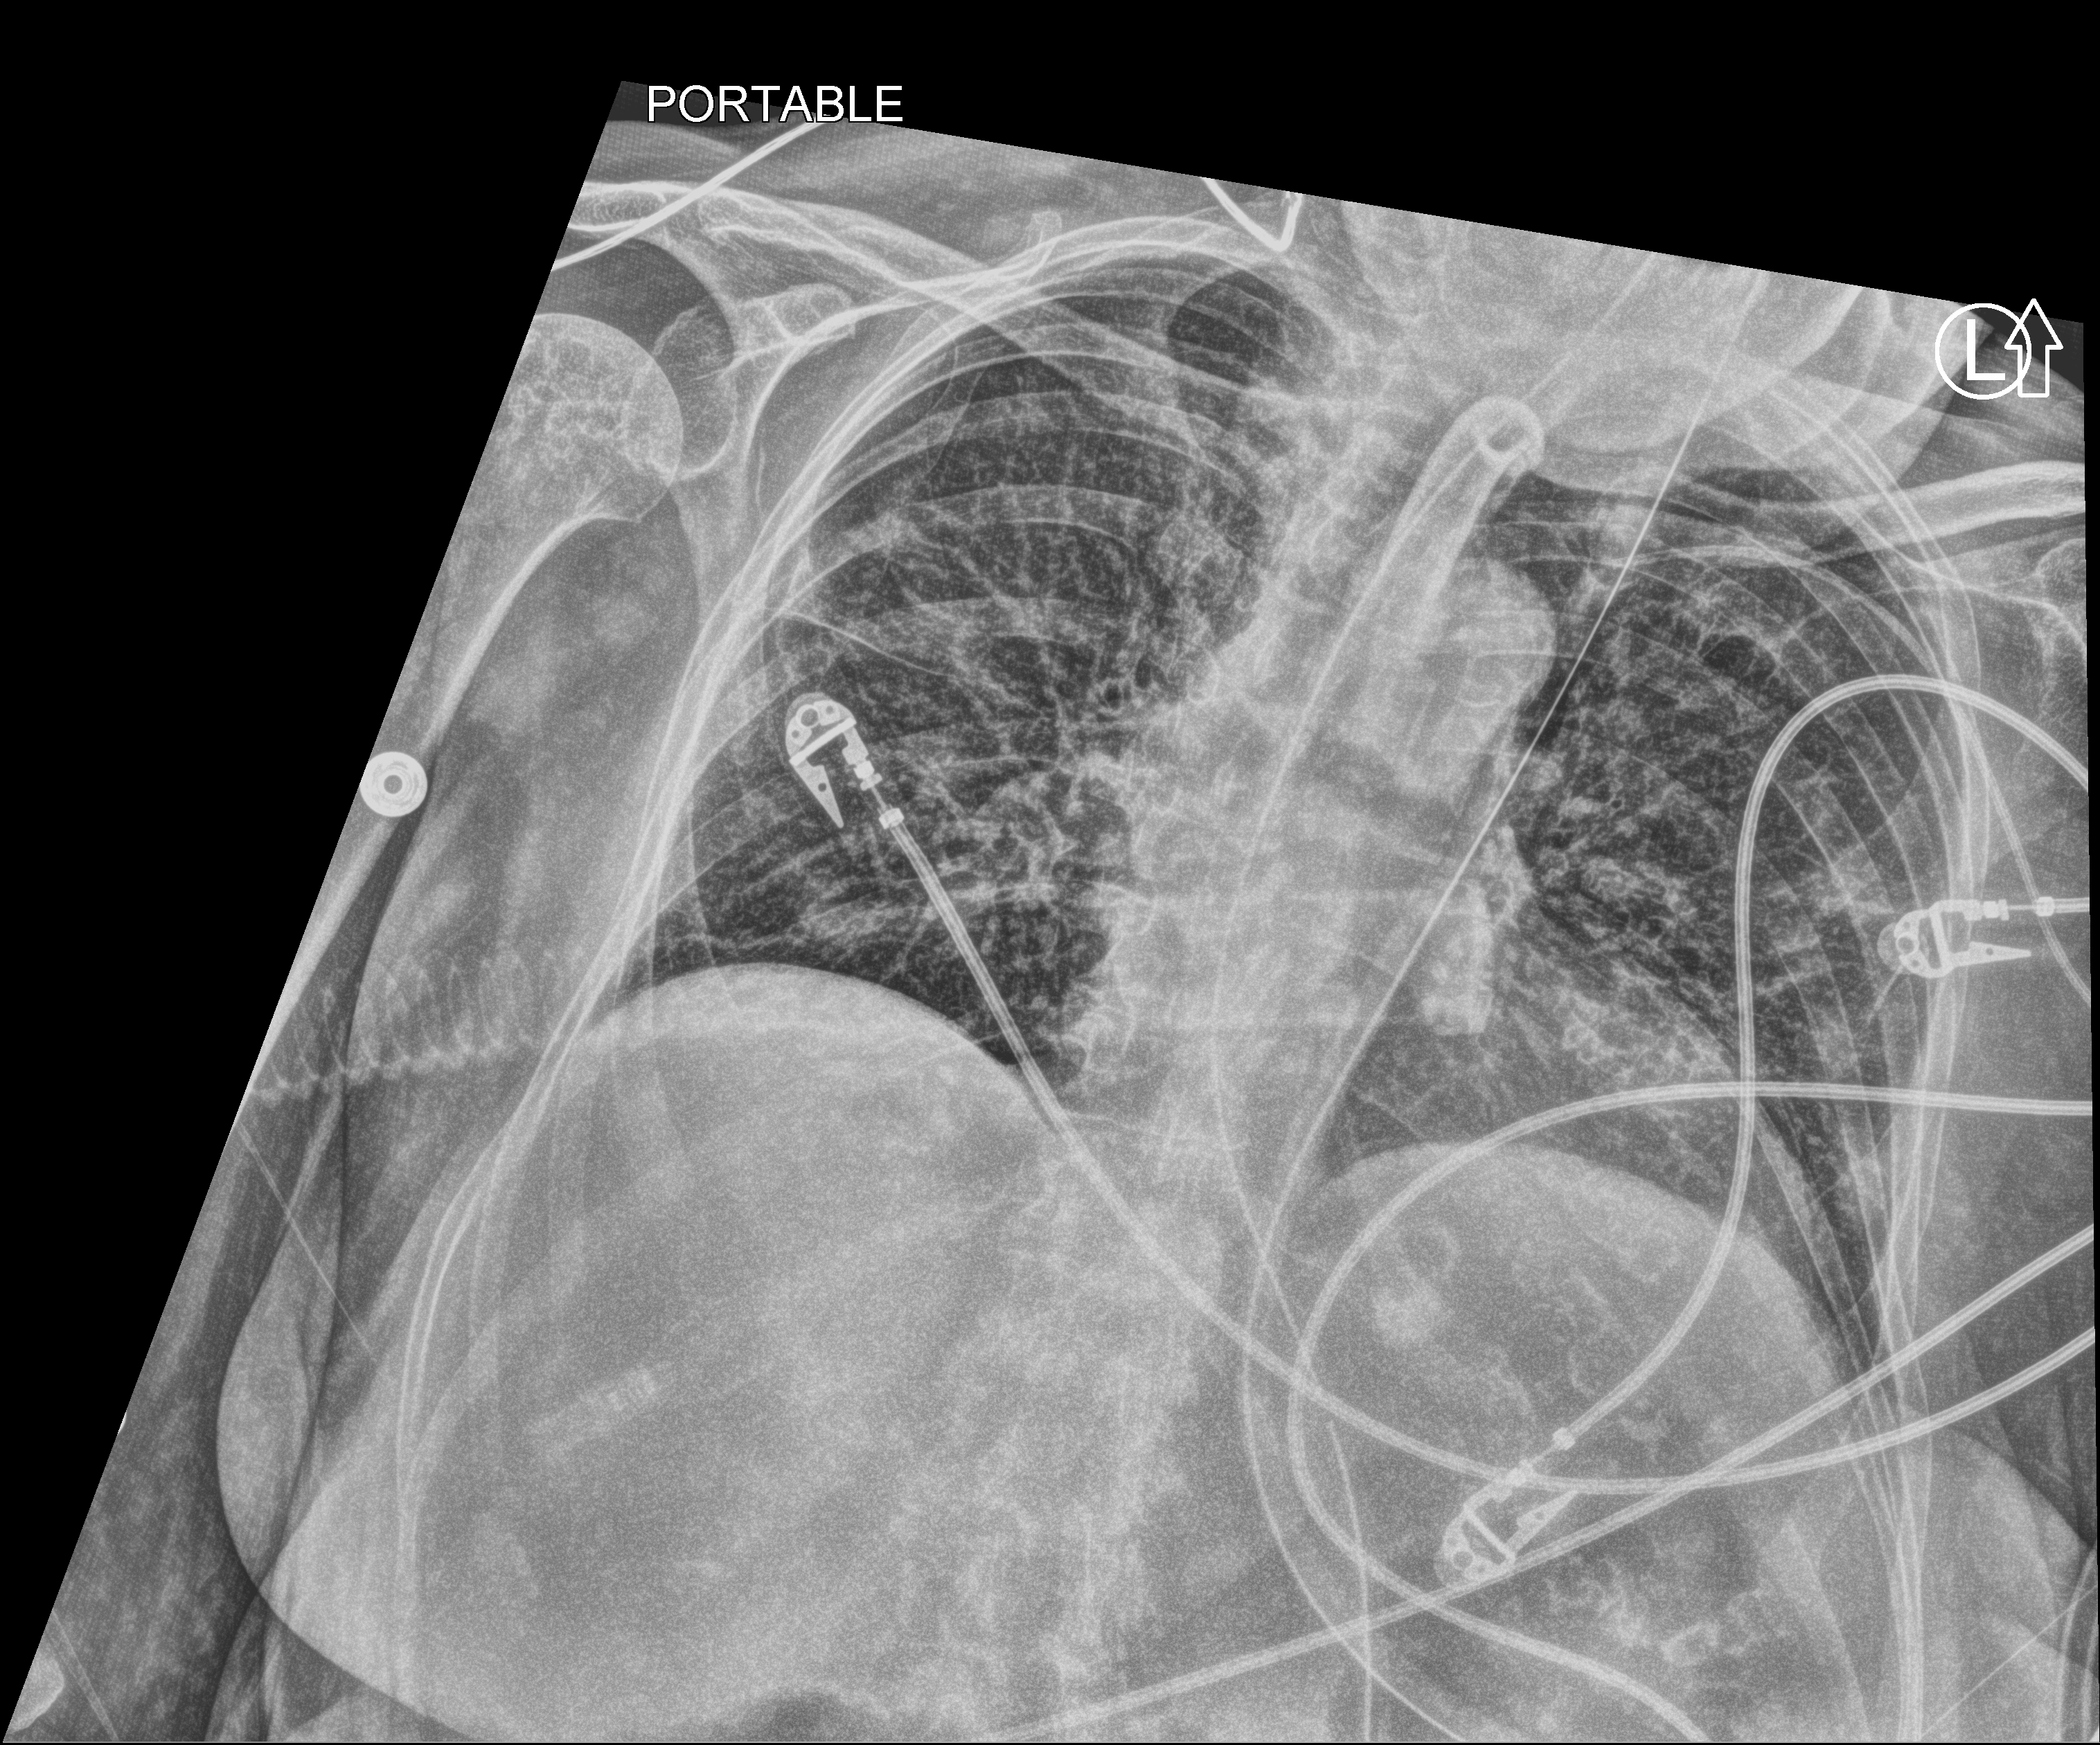
Chest X-ray (portable), anteroposterior (AP) projection. Patient hospitalised with COVID-19; female, aged 75–90 years.
Hospital-stay facts (about this admission, not read from this image; timing relative to this image not recorded): admitted to intensive care during this hospital stay: yes.